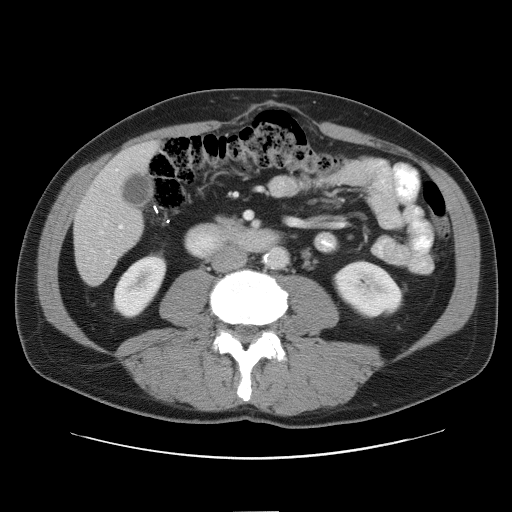
Contrast-enhanced abdominal CT, one axial slice; 120 kVp; intravenous contrast given; soft-tissue window (W 400 / L 40 HU); 5 mm slice thickness; 512 × 512 image matrix. Male patient, age 70 years. From the clinical record (not read from this slice): diagnosis: colorectal cancer liver metastases, imaged before liver resection.
Annotated regions visible in this slice (outlined manually by an expert reader):
- hepatic veins: bounding box [x1, y1, x2, y2] px = [100, 231, 103, 234]
- liver: [74, 142, 156, 285]
- planned liver remnant (the part of the liver to remain after resection): [120, 142, 156, 174]
- portal vein (with intrahepatic branches): [119, 224, 123, 229]